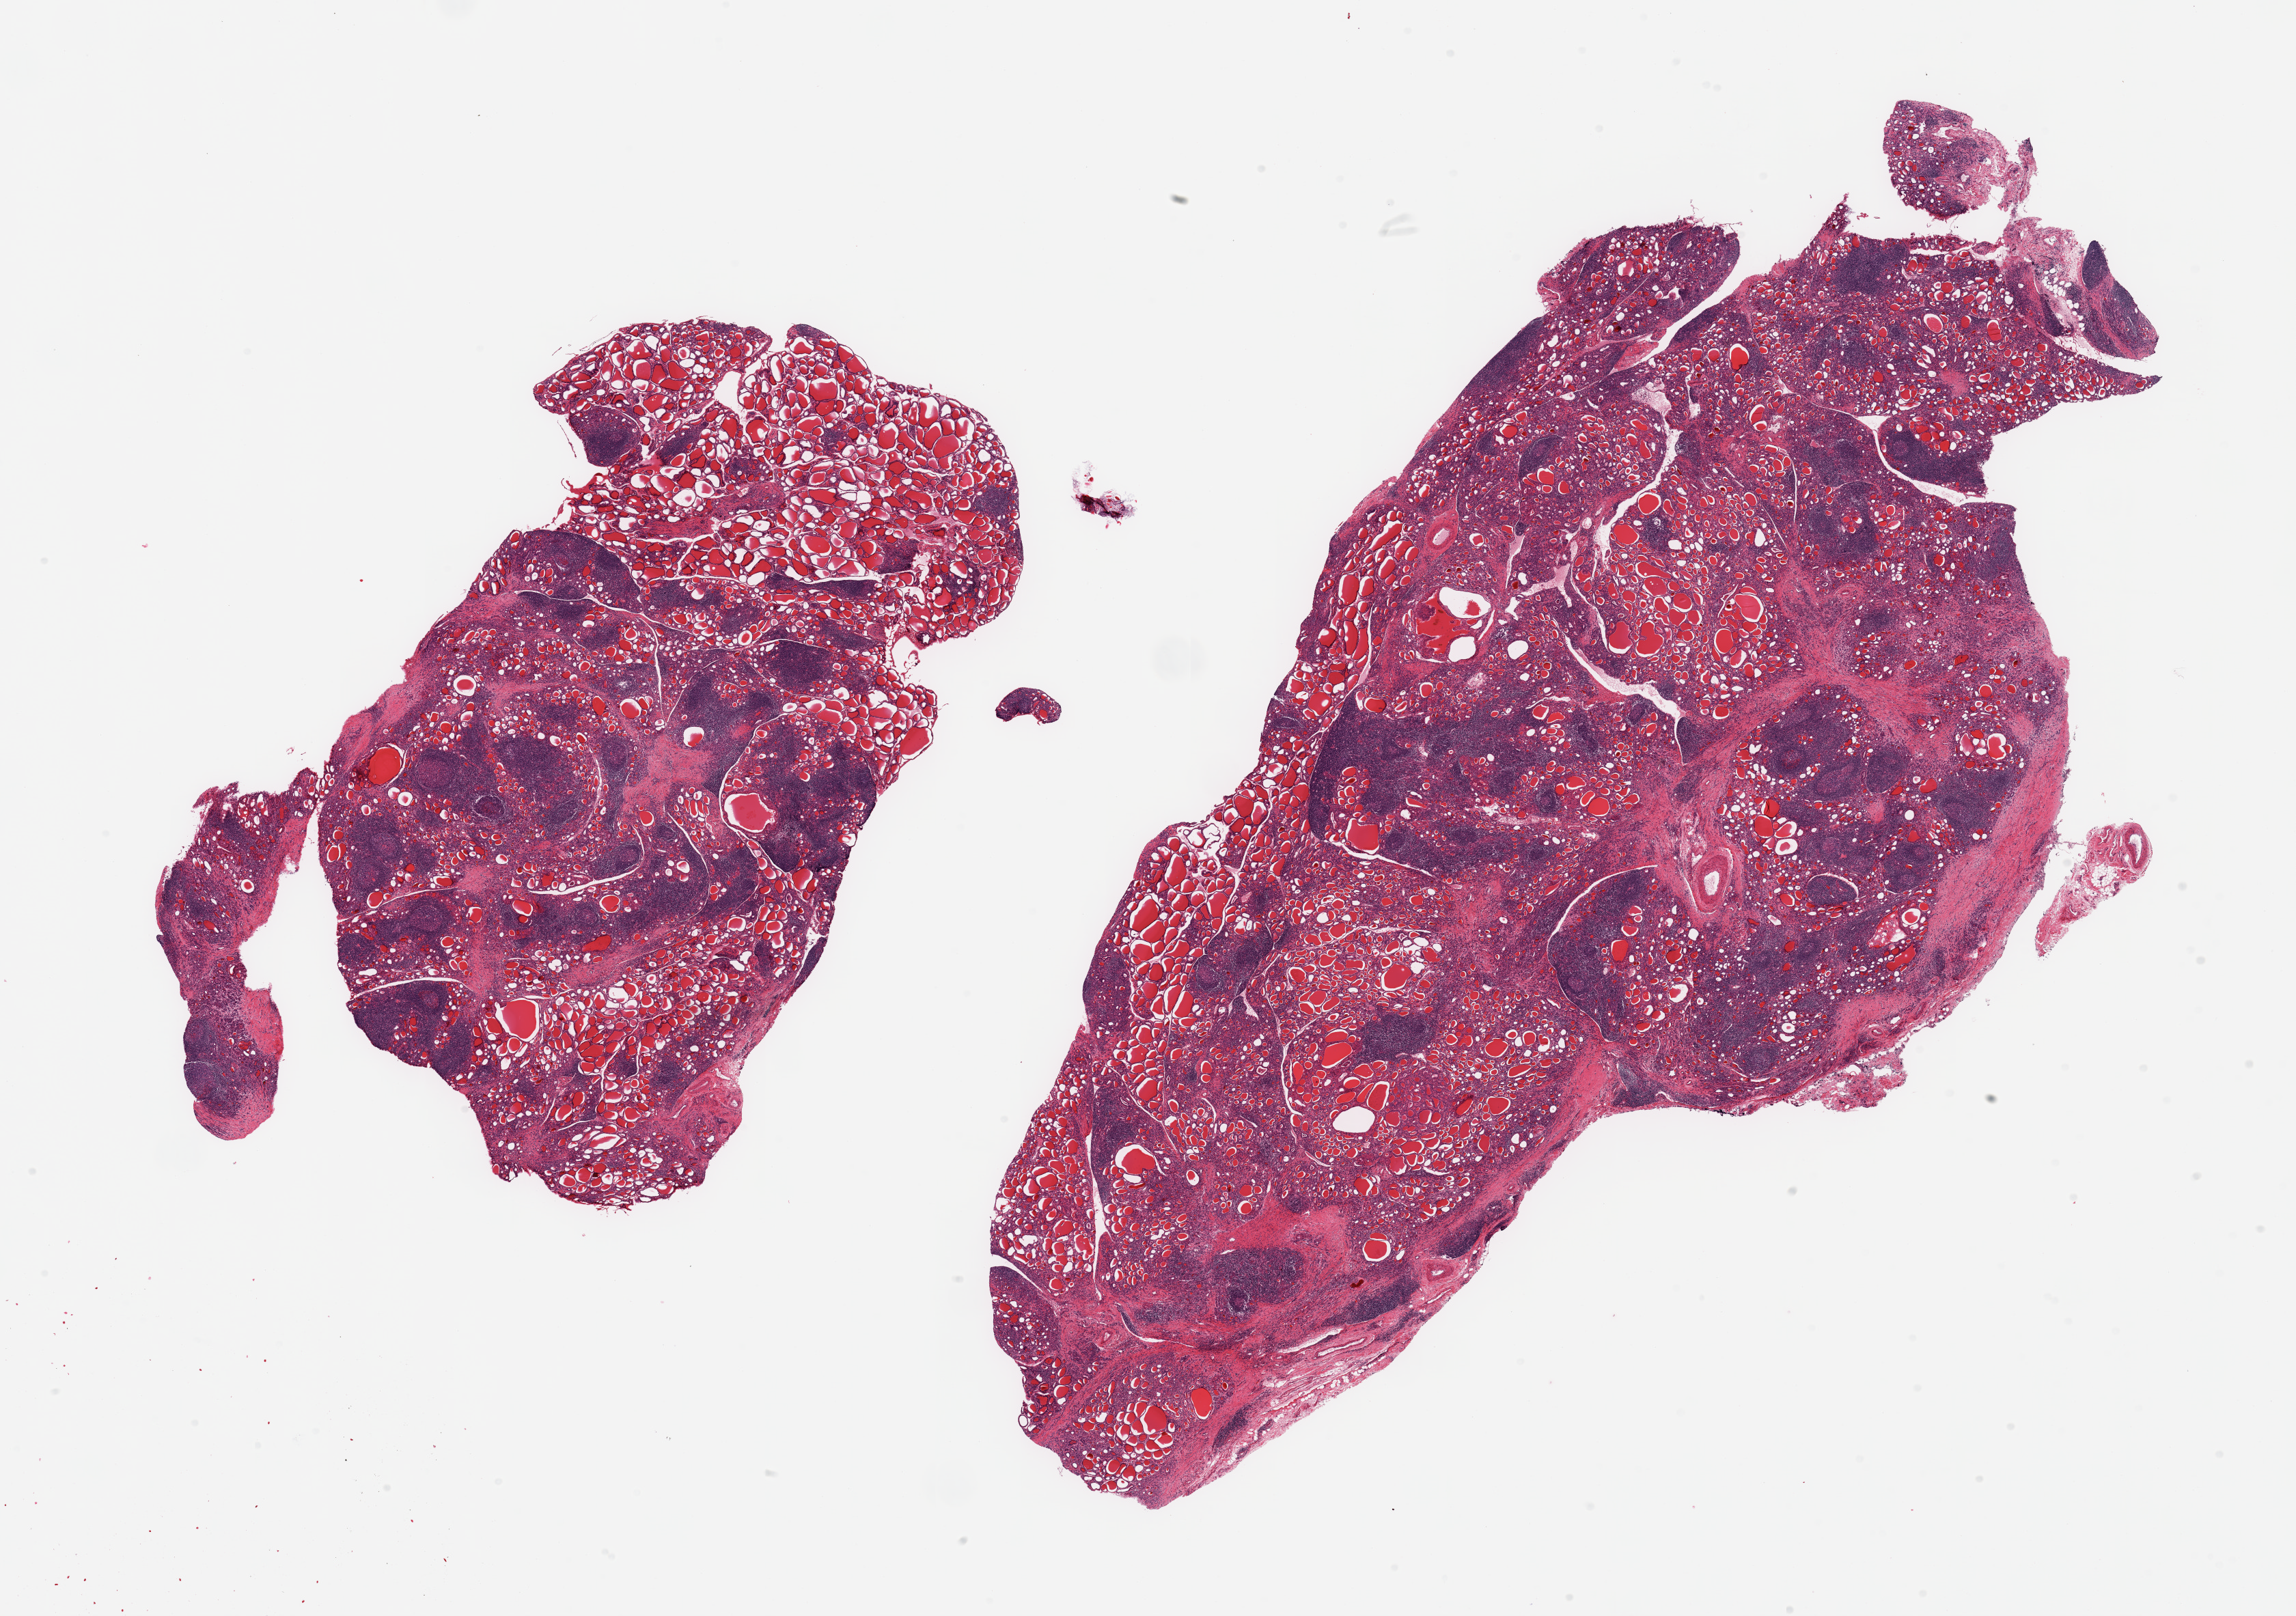
Whole-slide image, H&E stain — whole scanned area (about 26.6 x 18.7 mm, slide scanned at 20x) shown as a low-resolution overview. PAXgene-fixed, paraffin-embedded tissue. Sampled site (target tissue): thyroid. Tissue donor sample. Female donor.
Pathologist's review note for this sample: 2 pieces; extensive lymphocytic infiltrate with germinal center formation, fibrosis, and oncocytic change c/w Hashimoto's thyroiditis.